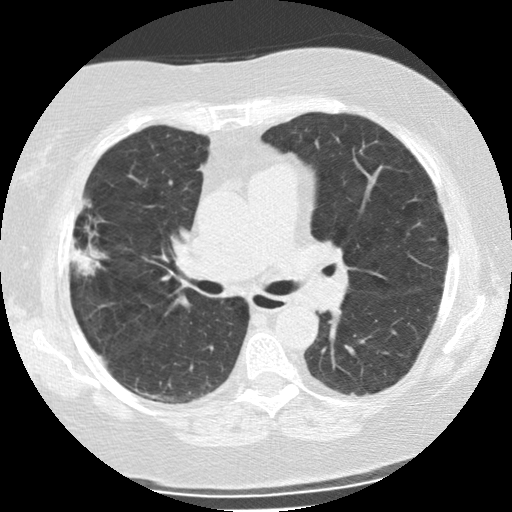
Low-dose screening chest CT, one axial slice; slice 136 of 225 in the series (ordered by position); 120 kVp; lung window (W 1500 / L -600 HU); 2.5 mm slice thickness; 512 × 512 image matrix, field of view 320 × 320 mm.
Structures marked on this image (expert manual segmentation):
- lesion 1 (tumor, upper lobe of right lung): box from (x=71, y=241) to (x=106, y=276) px